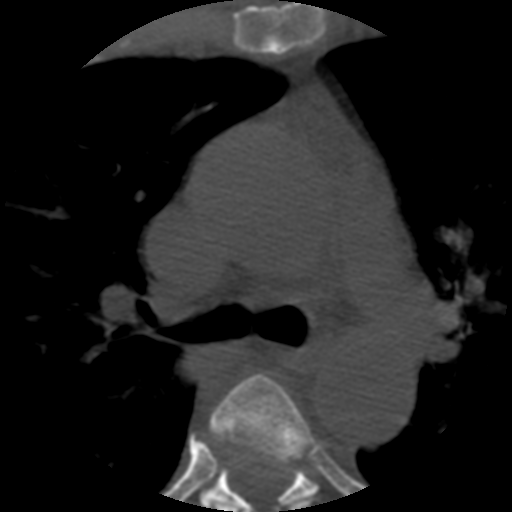
CT including the spine, one axial slice; position 385 of 508 along the scan axis; reconstruction kernel STANDARD; bone window (W 1800 / L 400 HU); 512 × 512 image matrix, field of view 160 × 160 mm. Patient age 57 years. Case-level facts recorded for this patient, not image findings: primary cancer: prostate.
Outlined on this slice (semi-automatically segmented with operator editing):
- T4 vertebra: bounding box <200,373,320,512> (left, top, right, bottom; pixels)
- T5 vertebra: <201,451,318,512>